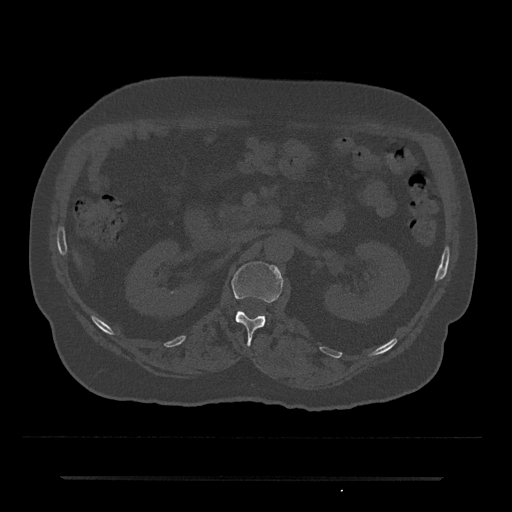
CT including the spine, one axial slice. Slice 62 of 797 in the series (ordered by position). Reconstruction kernel Br40s/3. 120 kVp. Bone window (W 1800 / L 400 HU). 512 × 512 image matrix, field of view 437 × 437 mm. Patient: male, 69 years. Case-level facts recorded for this patient, not image findings: primary cancer: prostate.
Outlined on this slice (semi-automatically segmented with operator editing):
- L1 vertebra: bounding box (x1, y1, x2, y2) in pixels: (232, 261, 283, 345)